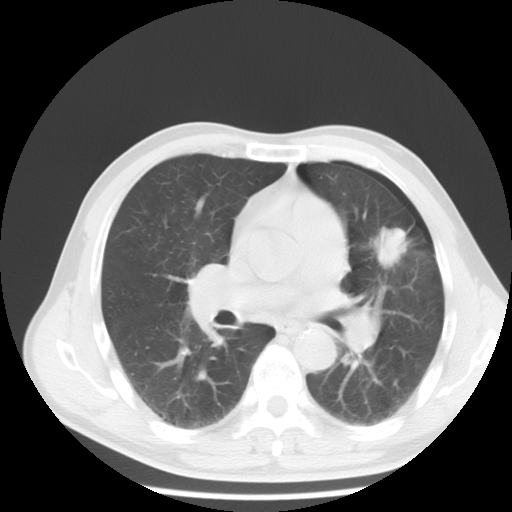
Chest CT, one axial slice. Position 5 of 9 along the scan axis. Lung window (W 1500 / L -600 HU). 5 mm slice thickness. 512 × 512 image matrix, field of view 350 × 350 mm. Patient: male, 54 years. From the clinical record (not read from this slice): clinical TNM (as recorded): T1c N0 M0.
Annotated regions visible in this slice (rectangle marked by the reading radiologist):
- lung tumour (recorded histology: adenocarcinoma): bounding box (x1, y1, x2, y2) in pixels: (375, 223, 412, 265)